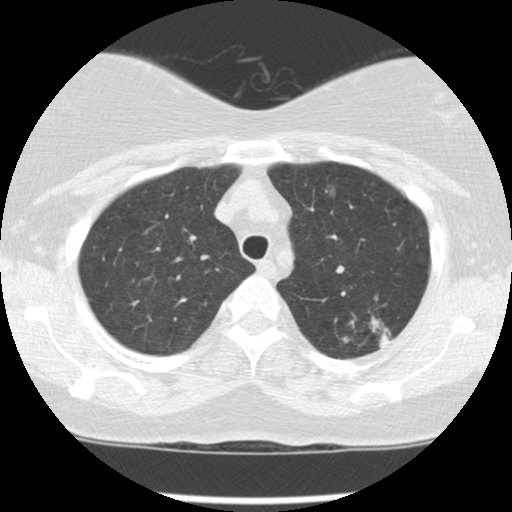
Chest CT (low-dose screening protocol), one axial image, third screening round (two years after baseline), lung window (W 1500 / L -600 HU), 2.5 mm slice thickness, standard (soft-tissue) reconstruction kernel (STANDARD), 120 kVp, slice 23 of 127 in the series. Female participant, aged 56 years at enrolment.
Lesion marked by an expert reader, bounding box <337,303,412,361> (left, top, right, bottom; pixels). The screening reader recorded 4 non-calcified nodules or masses ≥4 mm on this exam; which of them this box marks is not recorded. Official screen result: positive, other. Later outcome: lung cancer diagnosed 49 days after this screen — adenocarcinoma, NOS, left upper lobe, moderately differentiated (G2), stage IA (AJCC 6th edition), 10 mm at pathology.